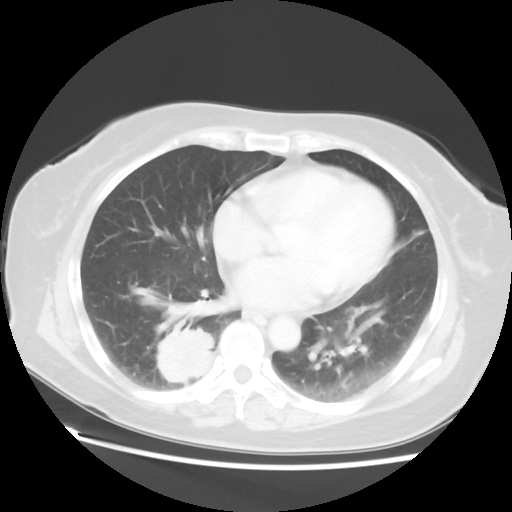
Chest CT, one axial slice. Position 24 of 52 along the scan axis. Reconstruction kernel STANDARD. 120 kVp. Lung window (W 1500 / L -600 HU). 5 mm slice thickness. 512 × 512 image matrix, field of view 356 × 356 mm. Female patient, age 69 years. From the clinical record (not read from this slice): clinical TNM (as recorded): T2 N1 M1a.
Structures marked on this image (bounding box drawn by a radiologist):
- lung tumour (recorded histology: adenocarcinoma): box from (x=151, y=321) to (x=216, y=389) px